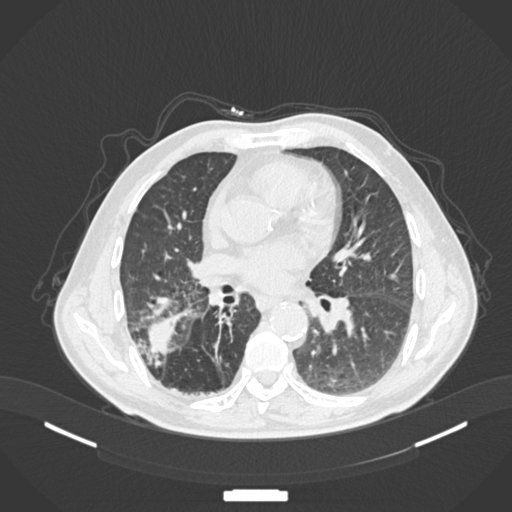
Chest CT, one axial slice; position 78 of 201 along the scan axis; reconstruction kernel B30f; lung window (W 1500 / L -600 HU); 1 mm slice thickness; 512 × 512 image matrix. Male patient, age 72 years. Case-level facts recorded for this patient, not image findings: clinical TNM (as recorded): T3 N2 M0.
Outlined on this slice (rectangle marked by the reading radiologist):
- lung tumour (recorded histology: adenocarcinoma): box from (x=143, y=314) to (x=177, y=358) px